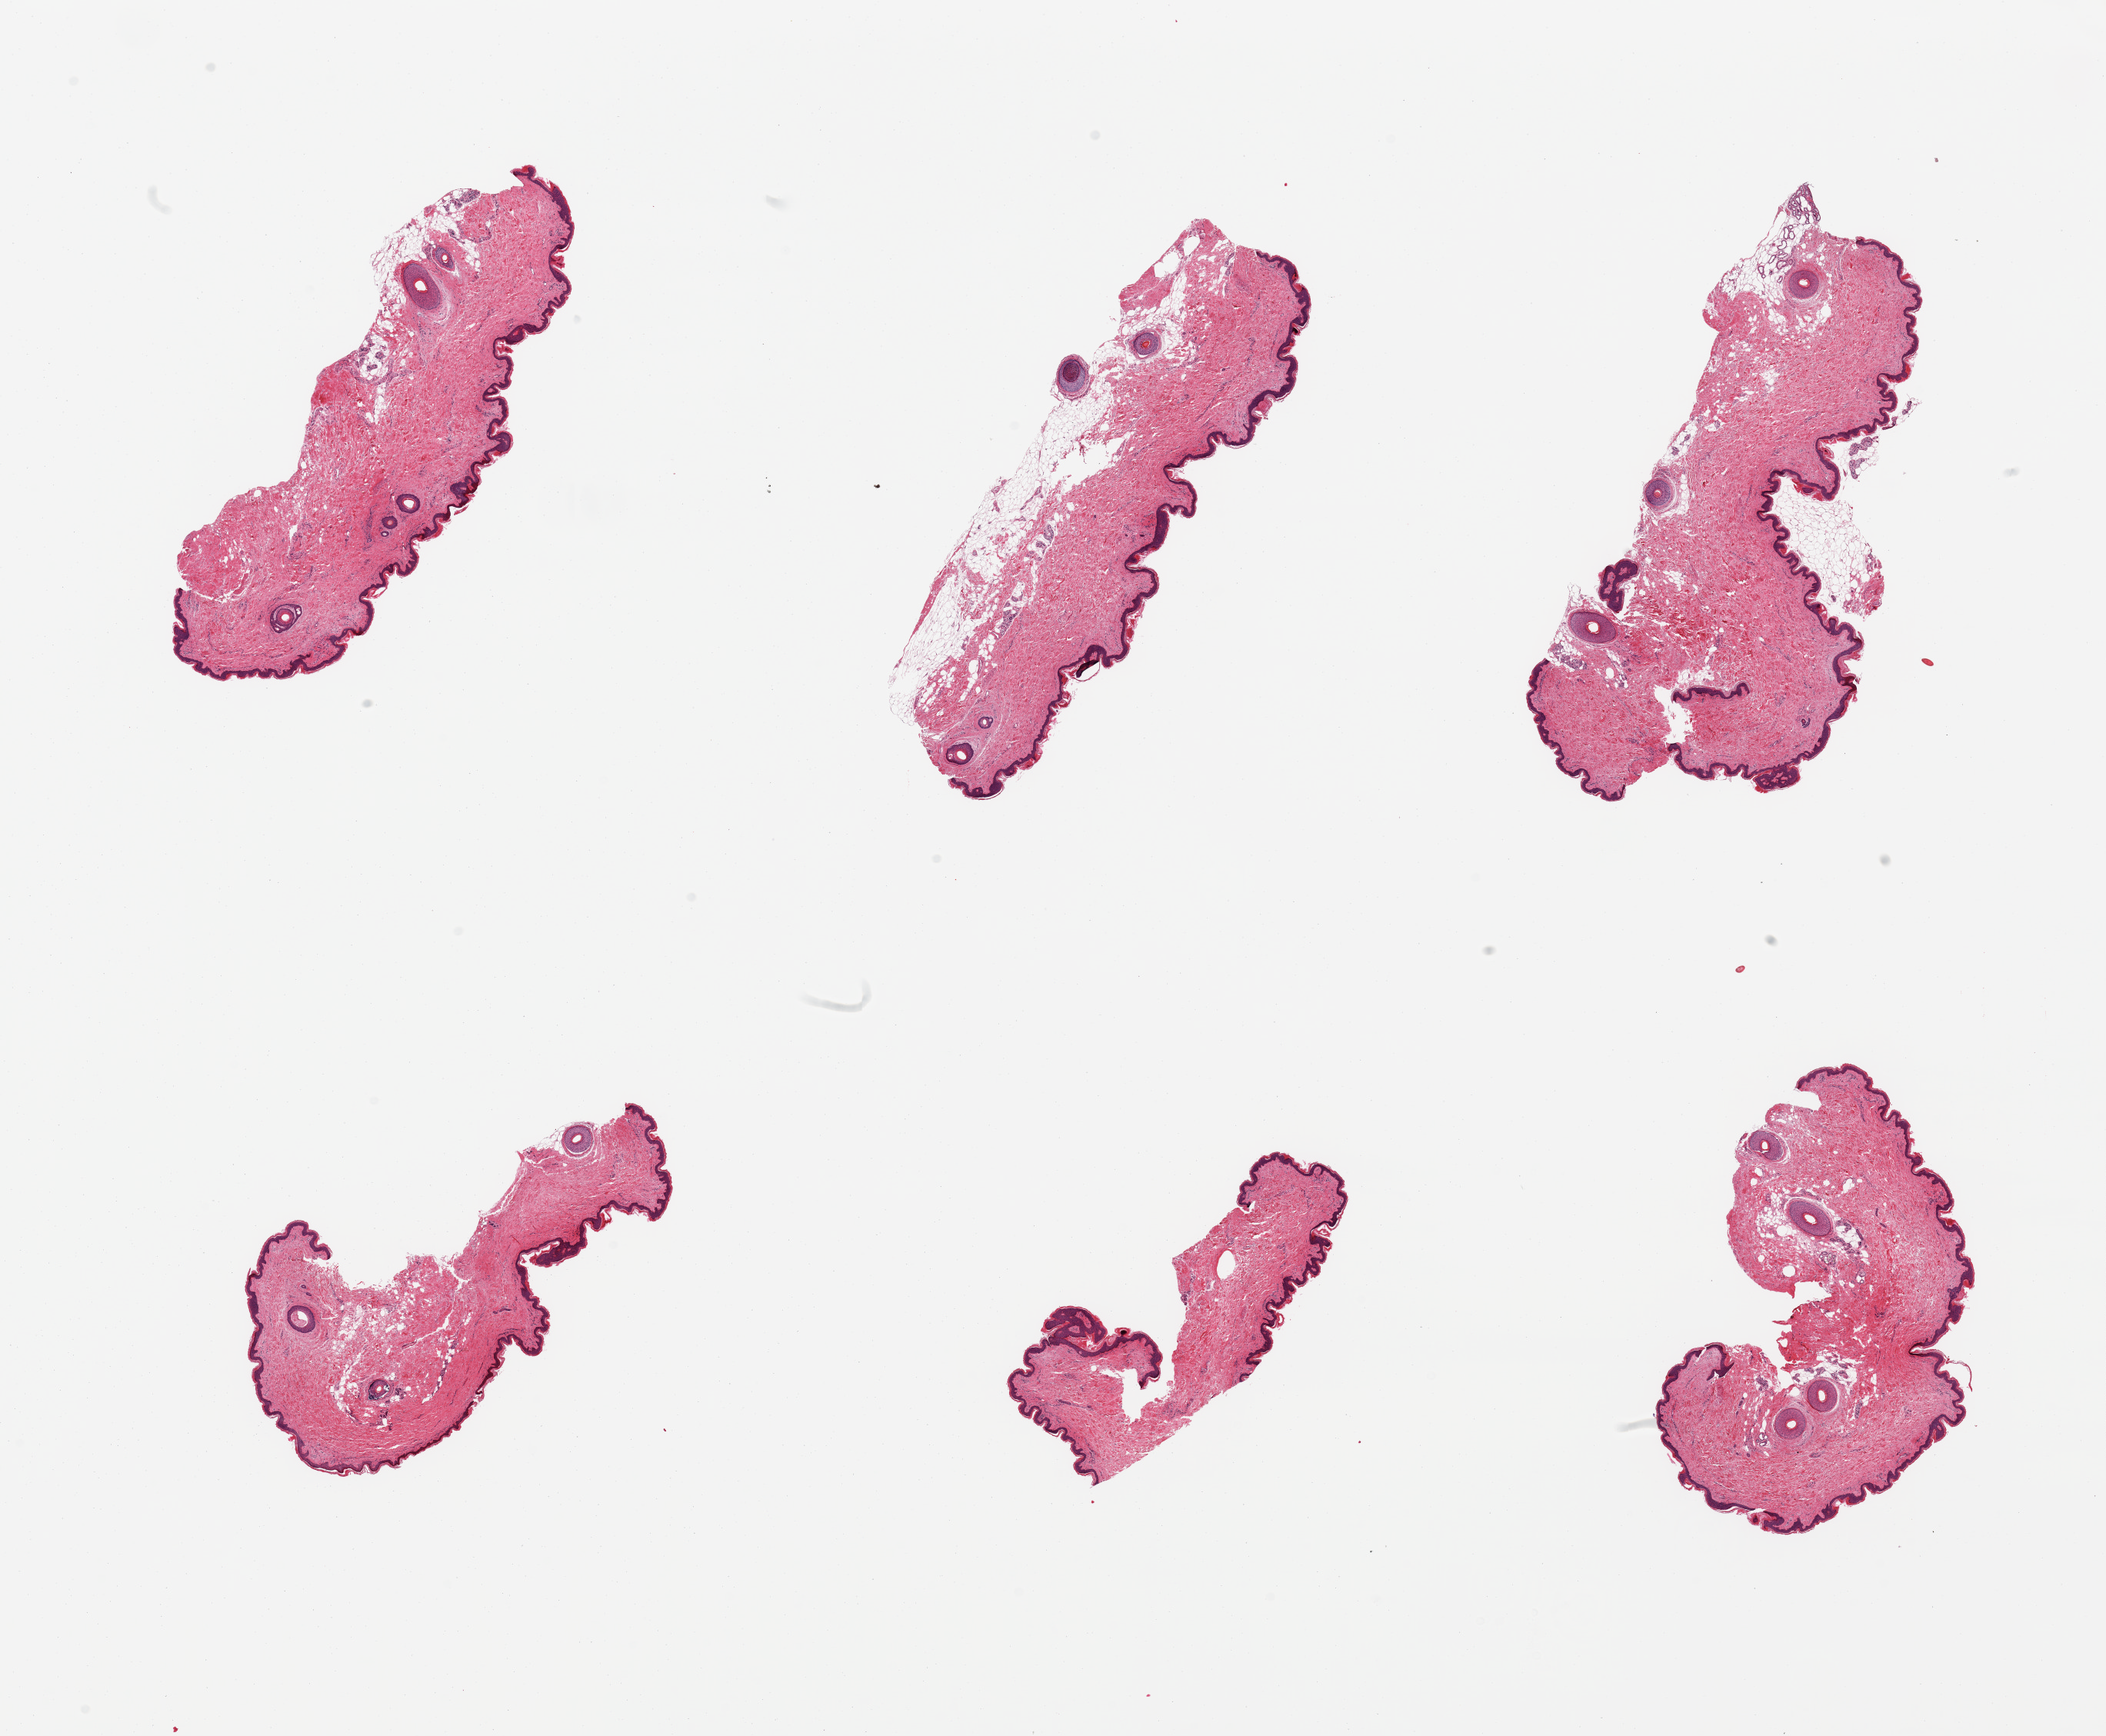
Haematoxylin and eosin whole-slide image, a low-resolution overview of the entire scanned area, about 21.7 x 17.9 mm. PAXgene-fixed paraffin-embedded (PFPE) section. Target tissue: skin of suprapubic region. Donor tissue sample.
Reviewer comment on this tissue sample: 6 pieces; scant to 30% dermal fat.